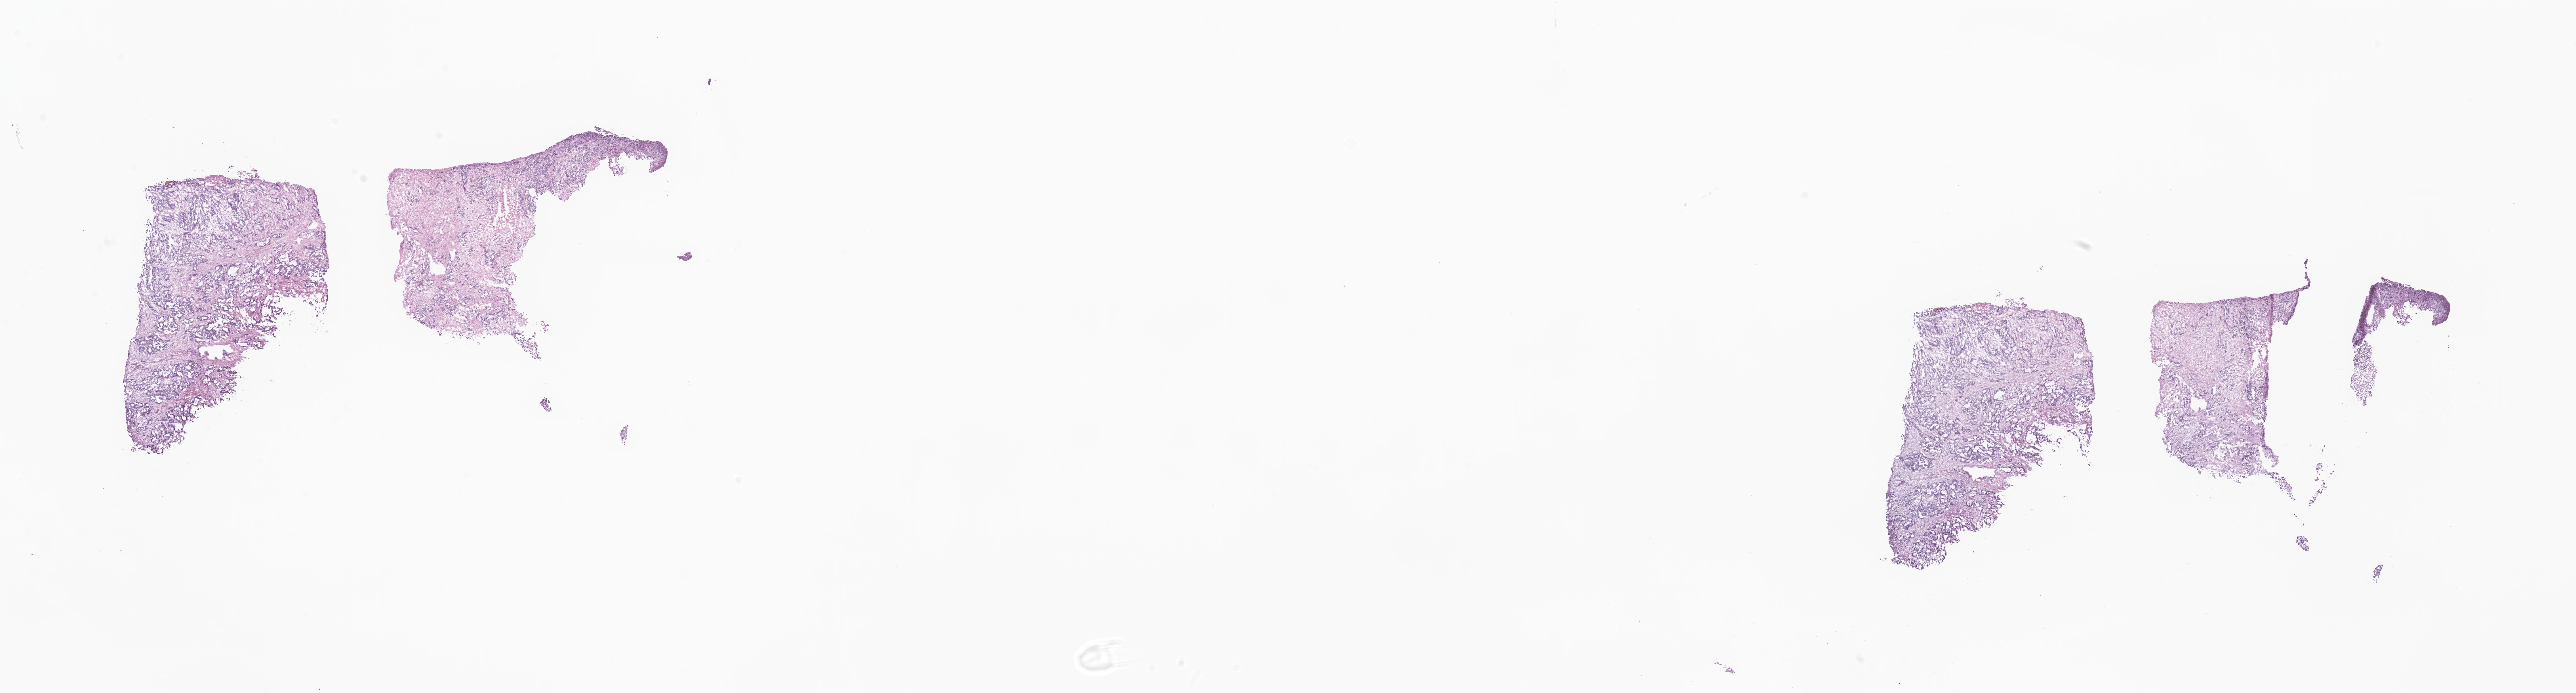
H&E whole-slide image, shown as a low-resolution overview of the whole scanned area (about 38.3 x 10.3 mm), frozen section (tissue freezing medium), metastatic tumor tissue, resected from liver. Male, age 65 years at initial diagnosis. Pathologist review of this section (percent, as recorded): tumor cells 85%, tumor nuclei 85%, stromal cells 15%, necrosis 0%, normal cells 0%. Inflammatory infiltration, as recorded: lymphocyte infiltration 4%, monocyte infiltration 1%, neutrophil infiltration 6%.
- section: bottom of the tissue portion
- patient diagnosis (primary): Adenocarcinoma, NOS